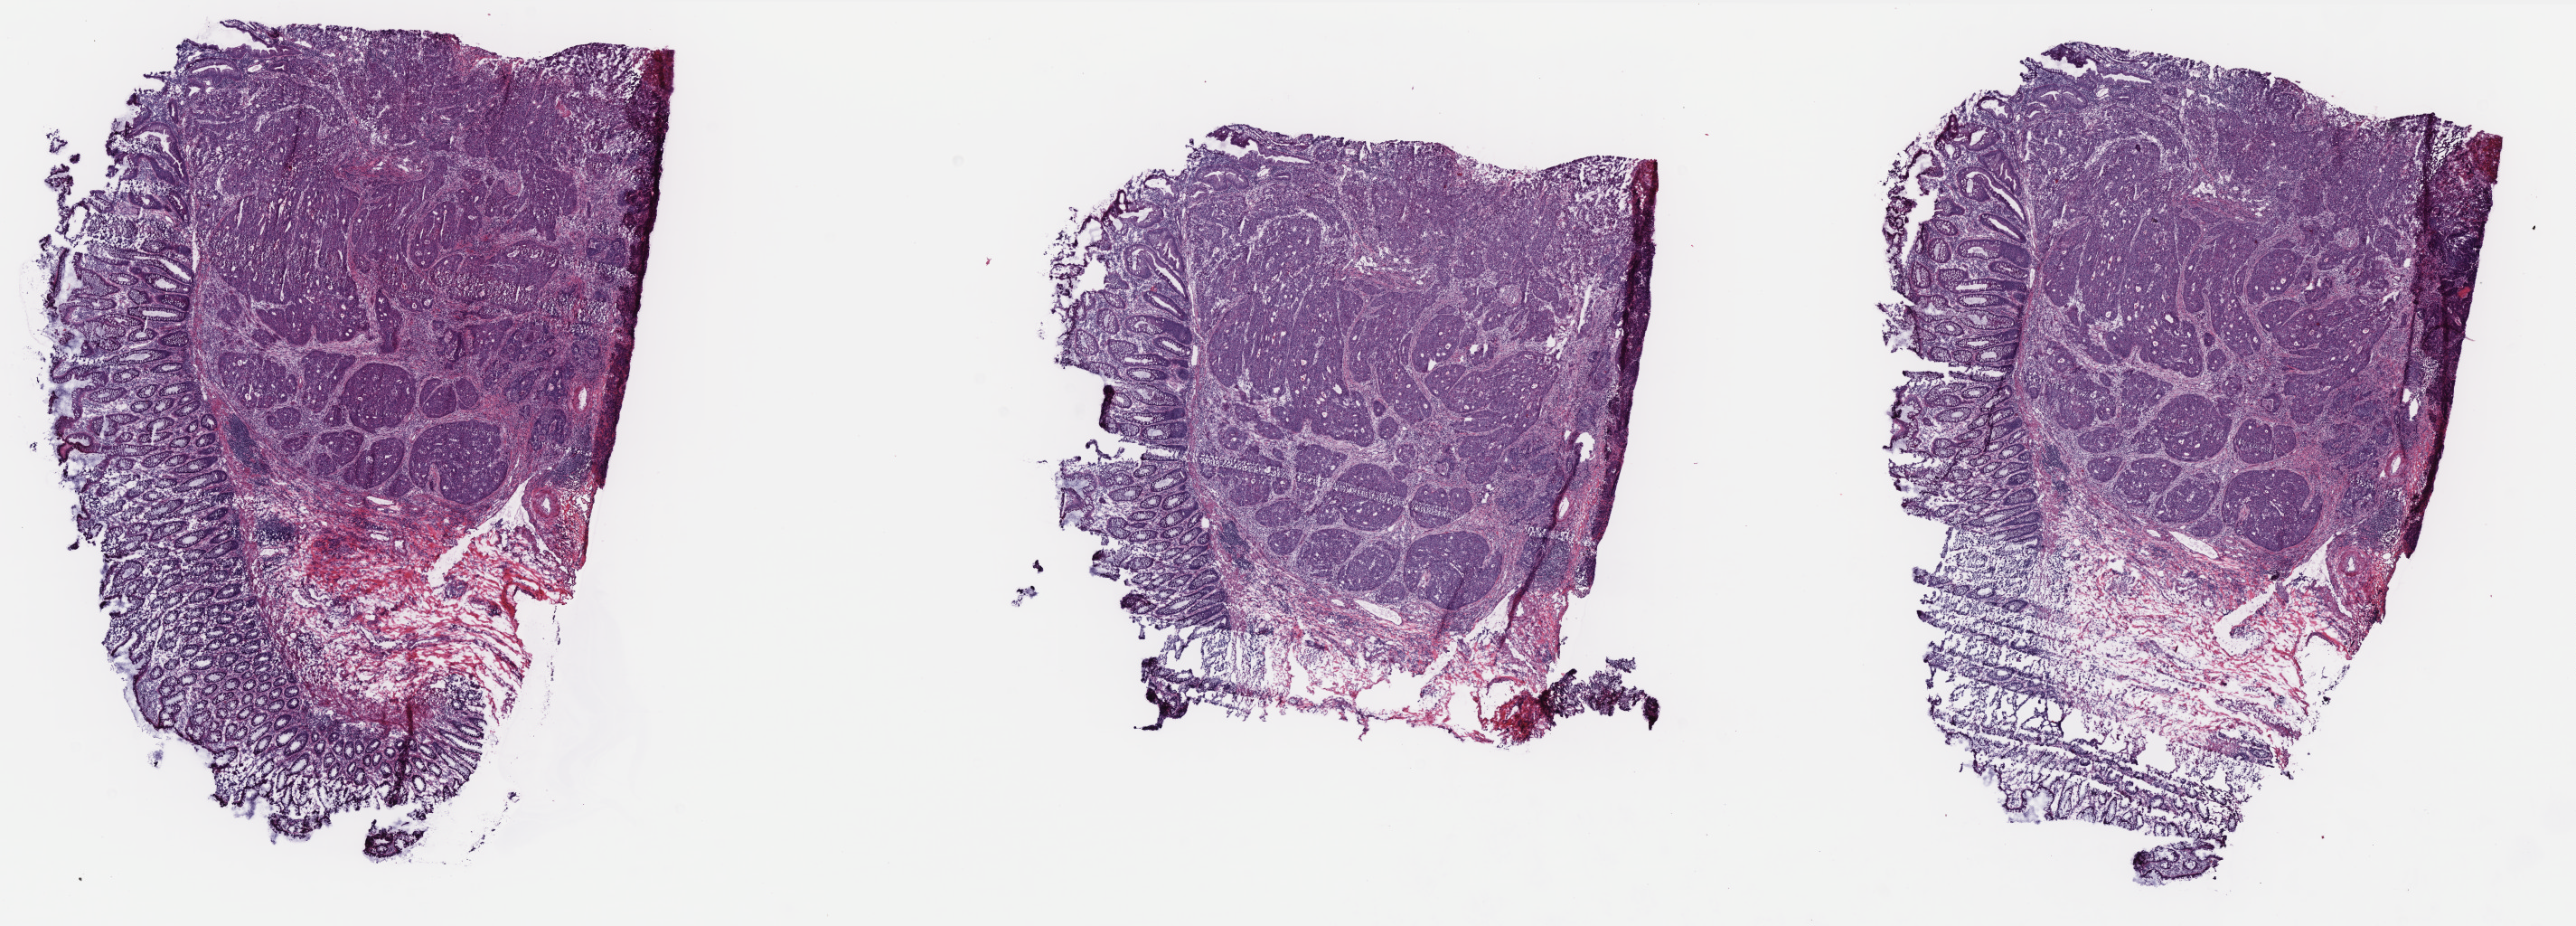
Digitized H&E-stained tissue section (whole slide), low-resolution overview of the scanned area, about 22.8 x 8.2 mm (acquisition: 40x scan); frozen section; sample: primary tumour, rectum. Male, age 80 years at initial diagnosis. Composition of this section per pathologist review: tumour cells 53%, tumour nuclei 70%, normal cells 44%, stromal cells 0%, necrosis 3%. Inflammatory infiltration, as recorded: lymphocyte infiltration 5%, monocyte infiltration 2%, neutrophil infiltration 2%.
AJCC pathologic stage: IIA (6th edition). Lymph nodes positive (case pathology): 0 of 14 examined. Diagnosis: Adenocarcinoma, NOS.